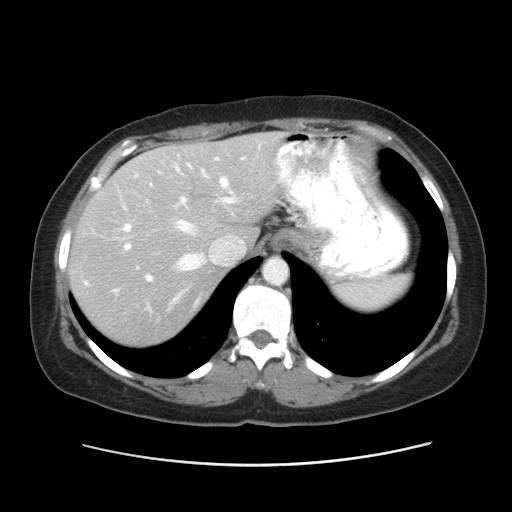
Contrast-enhanced abdominal CT, one axial slice. Slice 40 of 52 in the series (ordered by position). Reconstruction kernel STANDARD. Intravenous contrast given. Soft-tissue window (W 400 / L 40 HU). 5 mm slice thickness. 512 × 512 image matrix. Female patient, age 48 years. From the clinical record (not read from this slice): diagnosis: colorectal cancer liver metastases, imaged before liver resection; multiple liver metastases: yes; largest metastasis: 4.5 cm.
Structures marked on this image (manually delineated by an expert):
- hepatic veins: bounding box <114,147,259,311> (left, top, right, bottom; pixels)
- liver: <70,133,279,343>
- planned liver remnant (the part of the liver to remain after resection): <147,133,279,241>
- portal vein (with intrahepatic branches): <123,157,236,281>